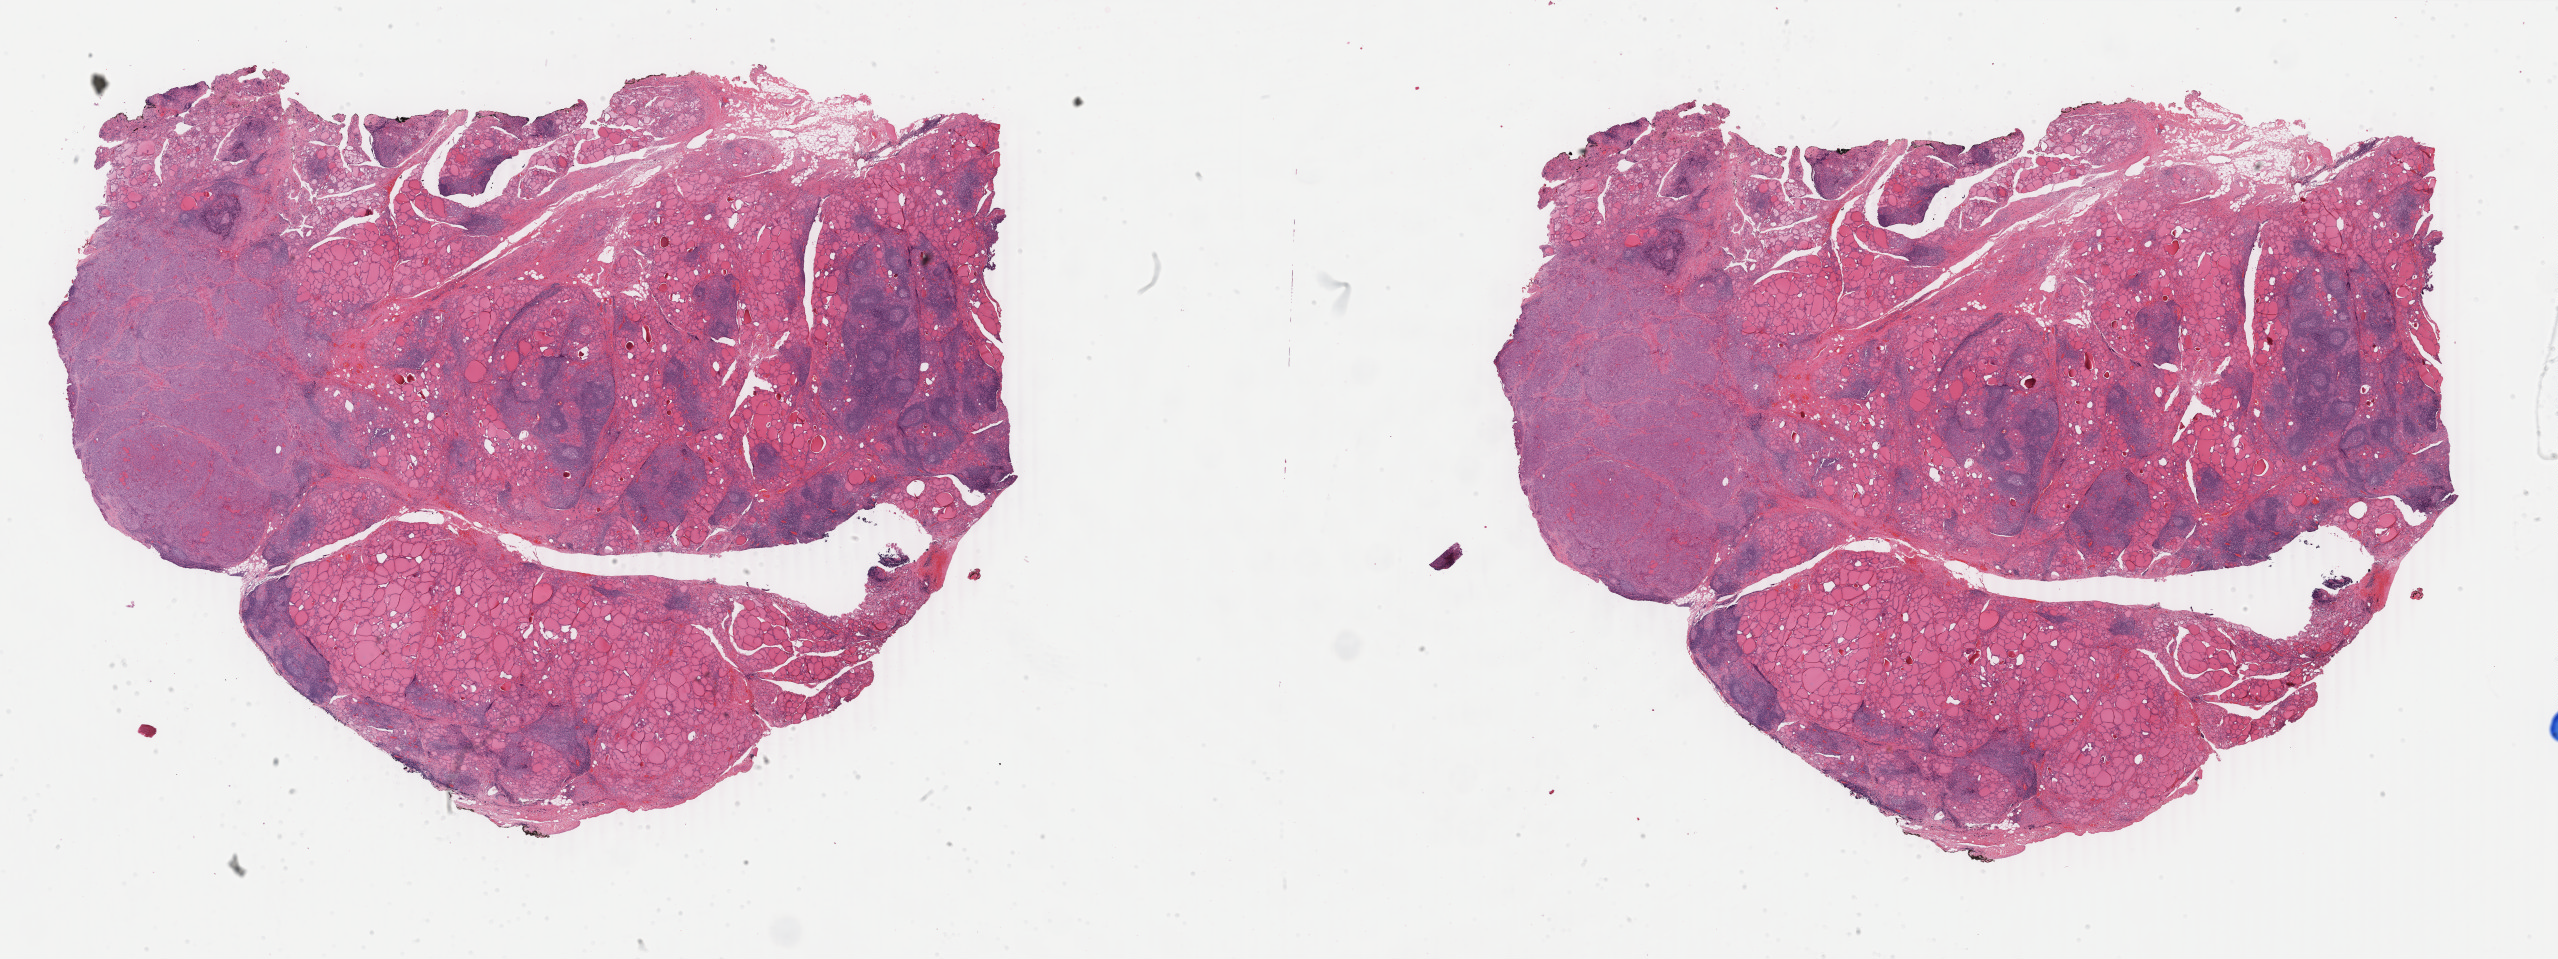
Whole-slide histology image, H&E, whole scanned area (about 40.7 x 15.3 mm) shown as a low-resolution overview. Formalin-fixed paraffin-embedded (FFPE) diagnostic section. Primary tumour sample from the thyroid. Patient: female, age at initial diagnosis 32 years.
* laterality: left
* diagnosis: Papillary carcinoma, columnar cell
* AJCC pathologic stage: I (7th edition)